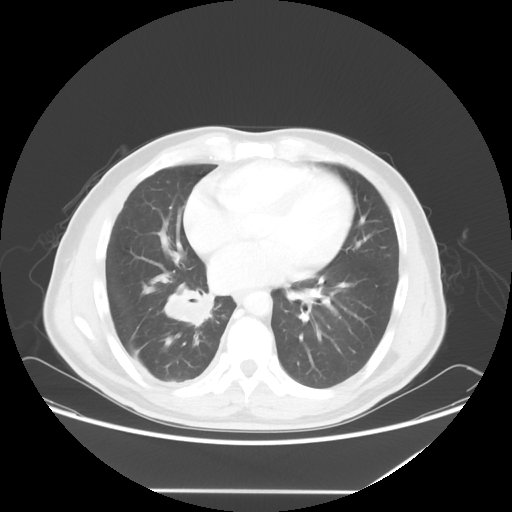
Chest CT, one axial slice; slice 25 of 60 in the series (ordered by position); 120 kVp; lung window (W 1500 / L -600 HU); 5 mm slice thickness; 512 × 512 image matrix. Male patient, age 48 years. Case-level facts recorded for this patient, not image findings: clinical TNM (as recorded): T3 N3 M1a.
Annotated regions visible in this slice (bounding box drawn by a radiologist):
- lung tumour (recorded histology: squamous cell carcinoma): bounding box <155,278,222,328> (left, top, right, bottom; pixels)